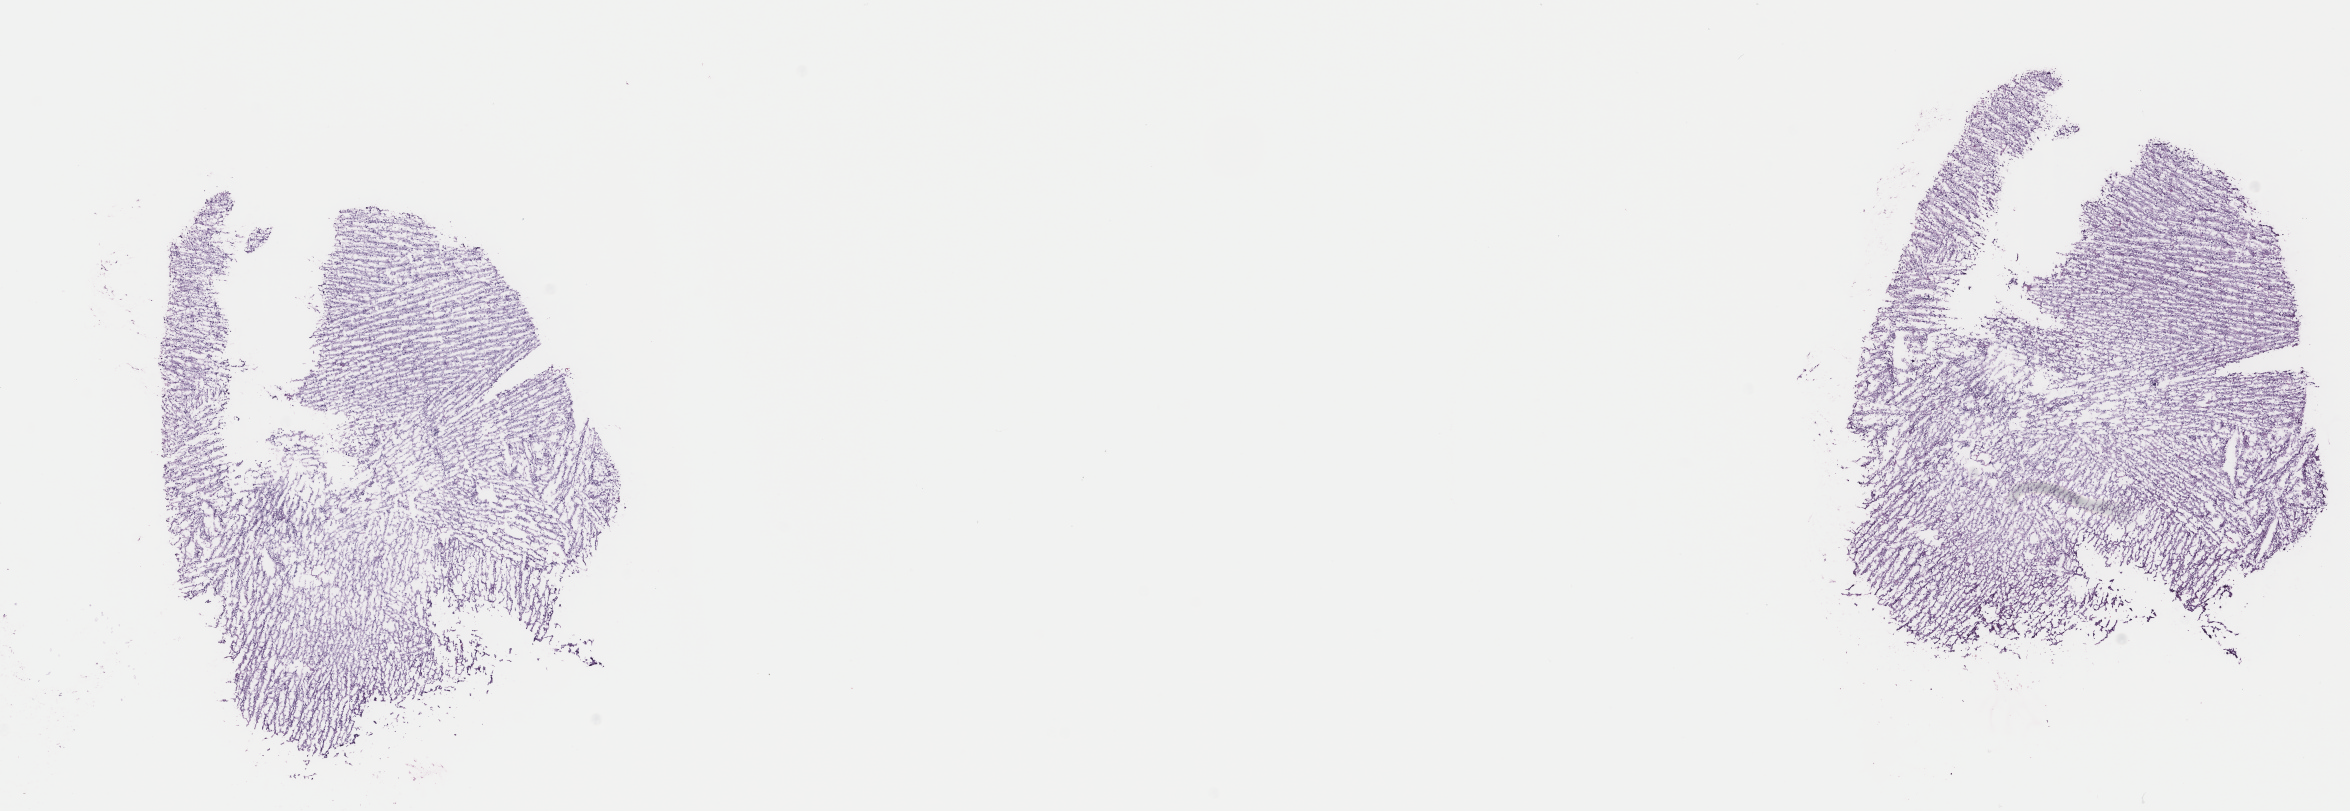
Whole-slide histology image, Hematoxylin and eosin (H&E) stained, whole scanned area (about 18.7 x 6.4 mm) shown as a low-resolution overview, frozen section from the top of the tissue portion, primary tumour sample from the brain. Patient: female, age at initial diagnosis 38 years. Histologic grade: G2 (moderately differentiated). Slide review estimates, as recorded: tumour cells 70%, tumour nuclei 90%, normal cells 5%, stromal cells 25%, necrosis 0%. Inflammatory infiltration, as recorded: lymphocyte infiltration 0%, monocyte infiltration 0%, neutrophil infiltration 0%.
* diagnosis: Oligodendroglioma, NOS